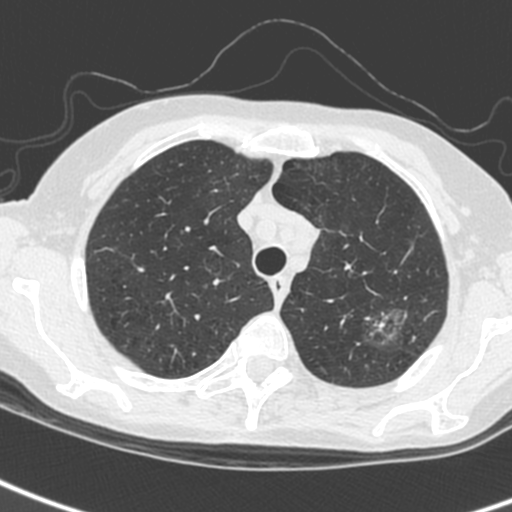
Axial slice from a low-dose chest CT screening exam, baseline annual screen, lung window (W 1500 / L -600 HU), standard (soft-tissue) reconstruction kernel (C), 120 kVp, slice 38 of 242 in the series. Female, age 61 years at enrolment. Current smoker at enrolment.
- Expert reader's lesion annotation, bounding box [x1, y1, x2, y2] px = [352, 304, 412, 351].
- The screening reader recorded 2 non-calcified nodules or masses ≥4 mm on this exam (left upper lobe, left upper lobe); which of them this box marks is not recorded.
- Official screen result: positive, change unspecified: nodule(s) >= 4 mm or enlarging nodule(s), mass(es), or other non-specific abnormalities suspicious for lung cancer.
- Later outcome: lung cancer diagnosed 29 days after this screen — small cell carcinoma, NOS, left upper lobe, stage IV (AJCC 6th edition).